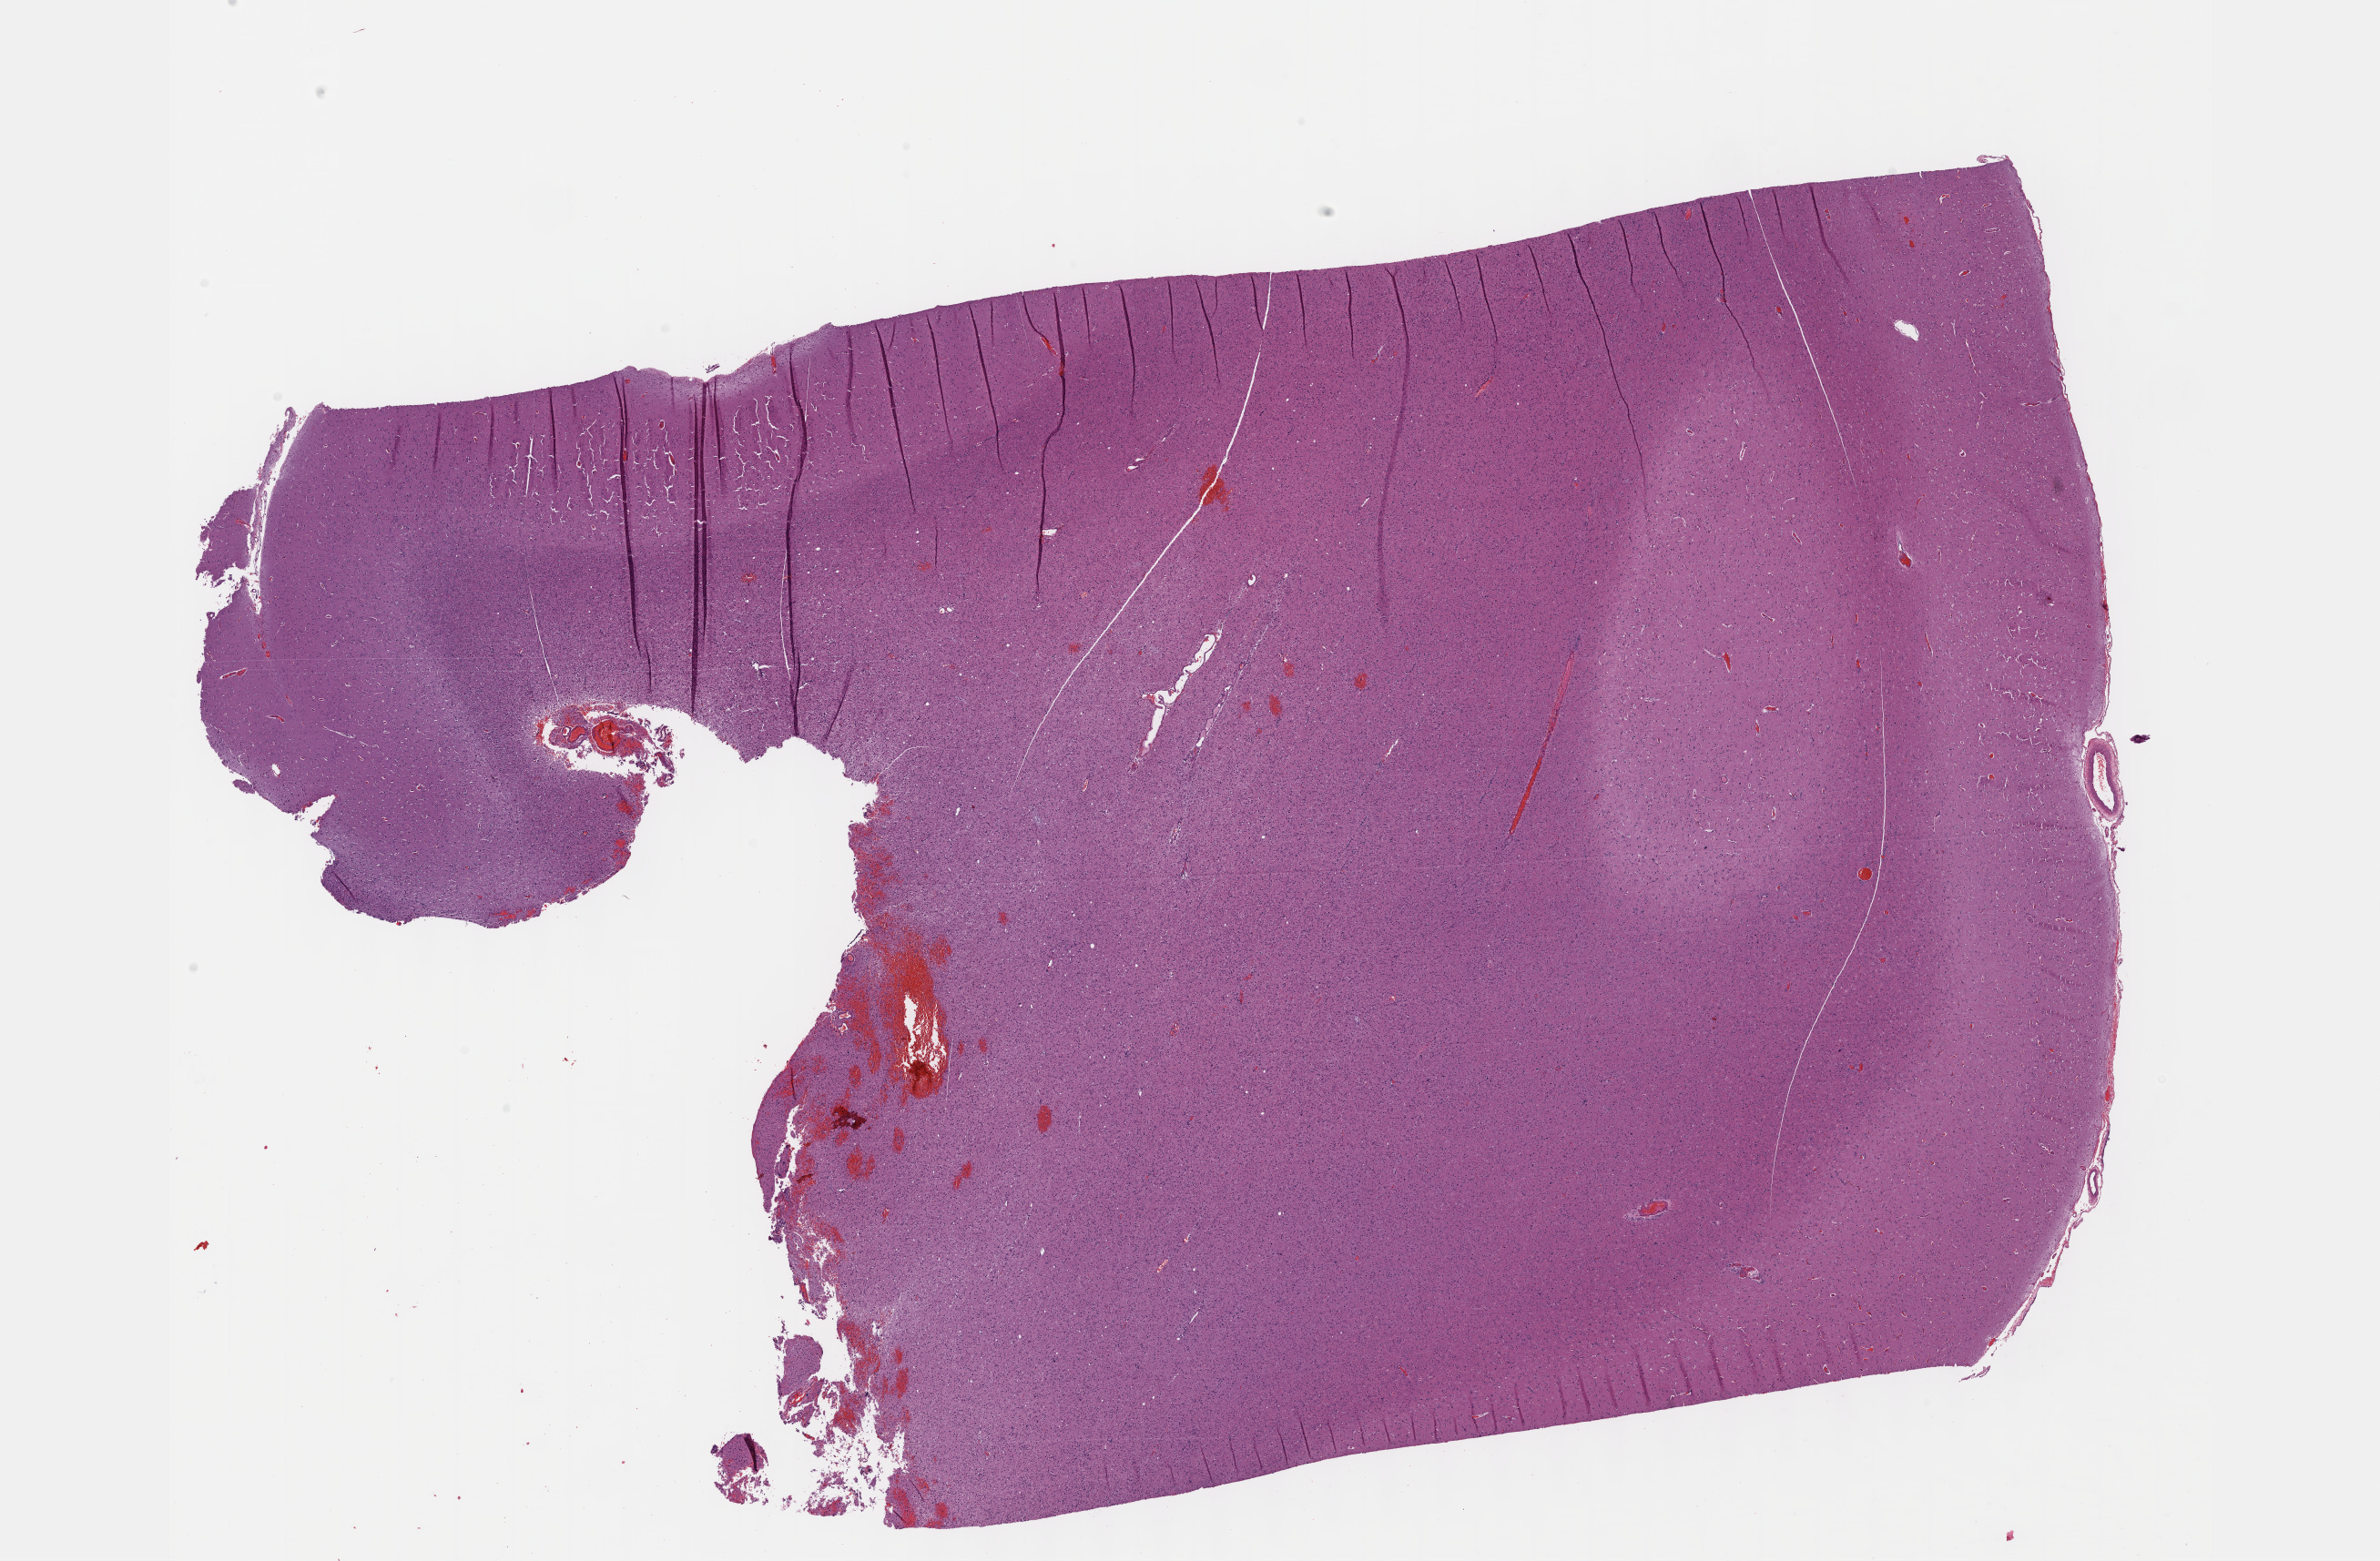
Digitized H&E-stained tissue section (whole slide) — a low-resolution overview of the entire scanned area, about 21.1 x 13.9 mm. FFPE section. Primary tumour sample from the brain. Male, age 59 years at initial diagnosis. Histologic grade: G3 (poorly differentiated).
• diagnosis: Oligodendroglioma, anaplastic (cerebrum)